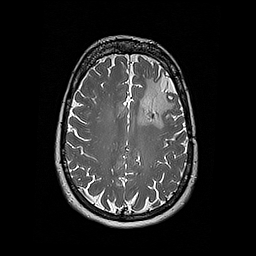
Brain MRI from a brain-tumour surgery series, one axial slice; position 125 of 192 along the scan axis; 1 mm slice thickness; 256 × 256 image matrix. From the clinical record (not read from this slice): histopathology: Oligodendroglioma; WHO grade: 2; IDH mutation: yes.
Annotated regions visible in this slice (expert manual segmentation):
- tumour: bounding box [x1, y1, x2, y2] px = [137, 77, 175, 129]